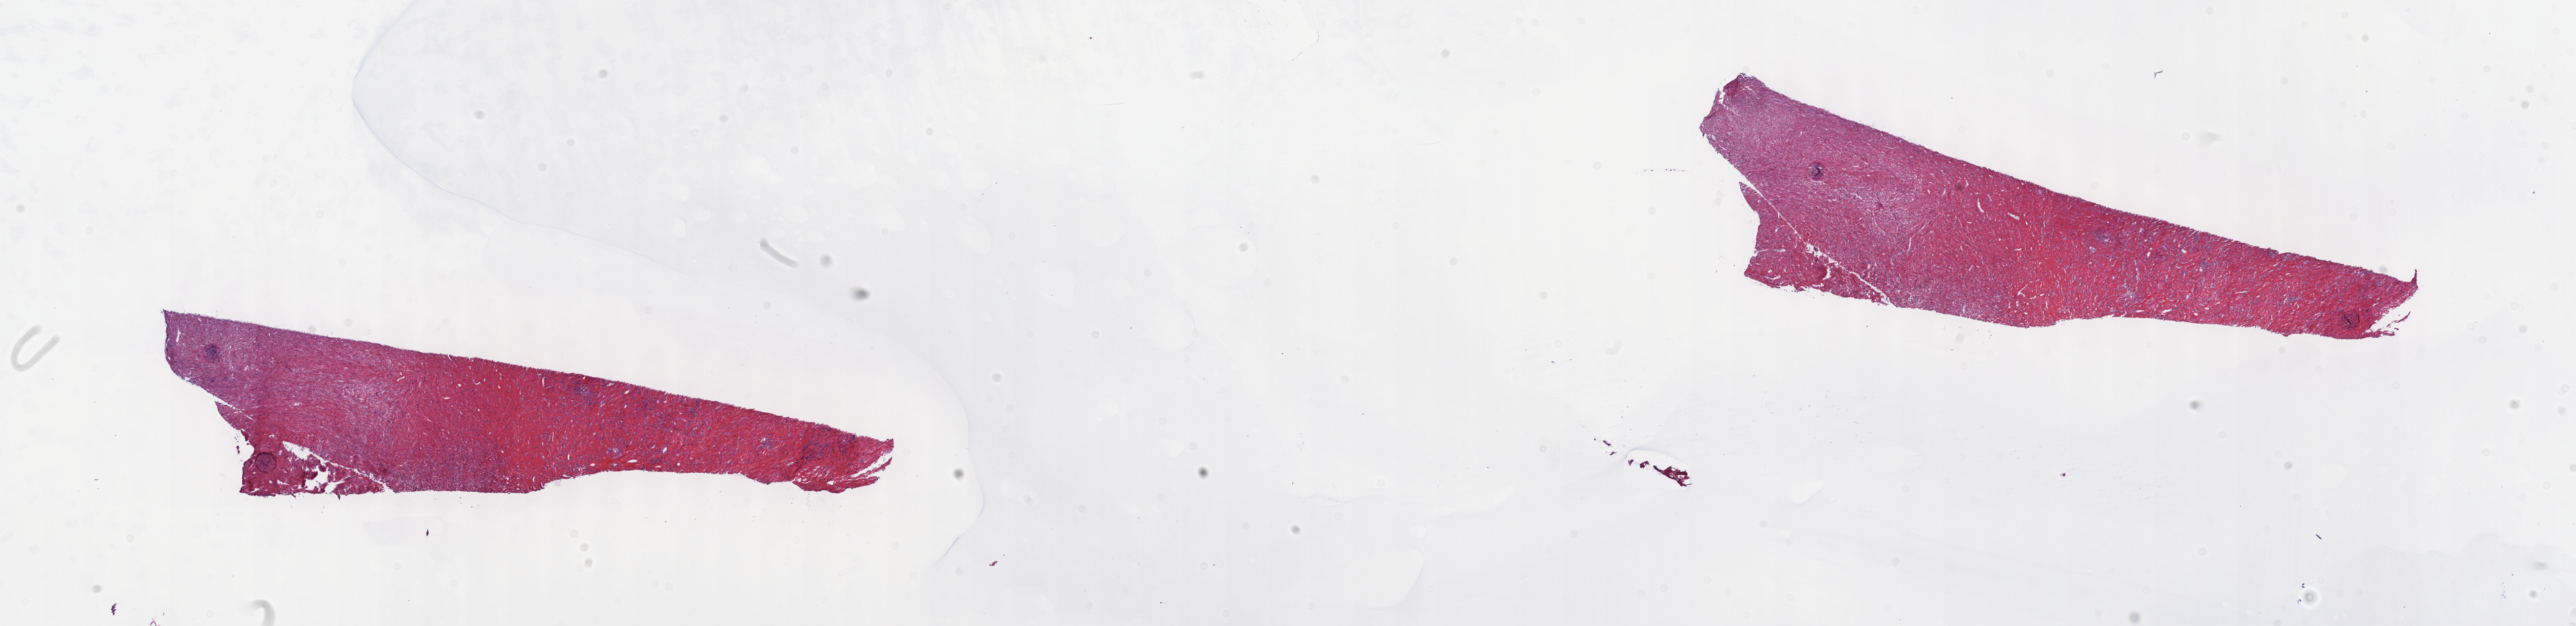
Whole-slide histology image, H&E, low-resolution overview of the scanned area, about 30.7 x 7.5 mm (from a 40x scan); frozen section from the top of the tissue portion; sample: primary tumour, retroperitoneum and peritoneum. Female patient; age at initial diagnosis 66 years. Composition of this section per pathologist review: tumour cells 100%, tumour nuclei 75%, normal cells 0%, stromal cells 0%, necrosis 0%. Infiltration values recorded for this section: lymphocyte infiltration 0%, monocyte infiltration 0%, neutrophil infiltration 0%.
* pathologic diagnosis: Dedifferentiated liposarcoma (retroperitoneum)